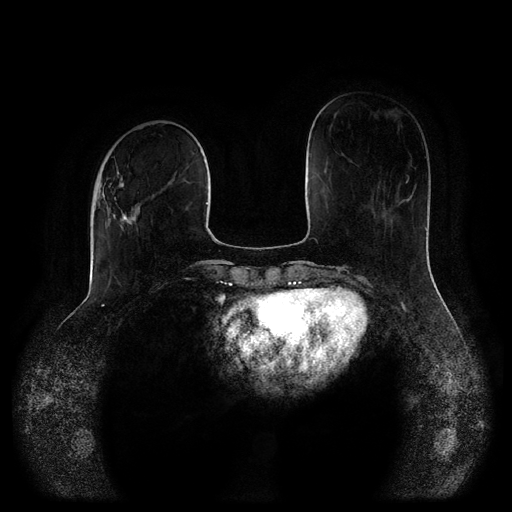
Breast MRI (dynamic contrast-enhanced, multi-phase), one axial slice. Position 32 of 116 along the scan axis. Dynamic contrast-enhanced series, time point 2 of 5 at this slice position (early post-contrast). 1.5 T. TE 2.6 ms, TR 5.2 ms. 2 mm slice thickness. 512 × 512 image matrix, field of view 380 × 380 mm. Female patient, age 52 years.
Structures marked on this image (semi-automatically segmented with operator editing):
- breast lesion (labelled 'tumour' in the annotation; benign lesions carry a separate 'benign' label): box from (x=98, y=171) to (x=145, y=237) px